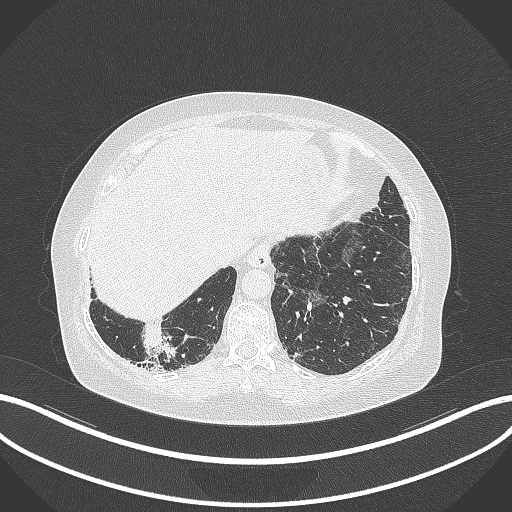
Chest CT, one axial slice; position 23 of 296 along the scan axis; reconstruction kernel B70f; 120 kVp; lung window (W 1500 / L -600 HU); 1 mm slice thickness; 512 × 512 image matrix. Female patient, age 65 years. Case-level facts recorded for this patient, not image findings: clinical TNM (as recorded): T2b N1 M0.
Outlined on this slice (rectangle marked by the reading radiologist):
- lung tumour (recorded histology: adenocarcinoma): bounding box <136,322,177,361> (left, top, right, bottom; pixels)